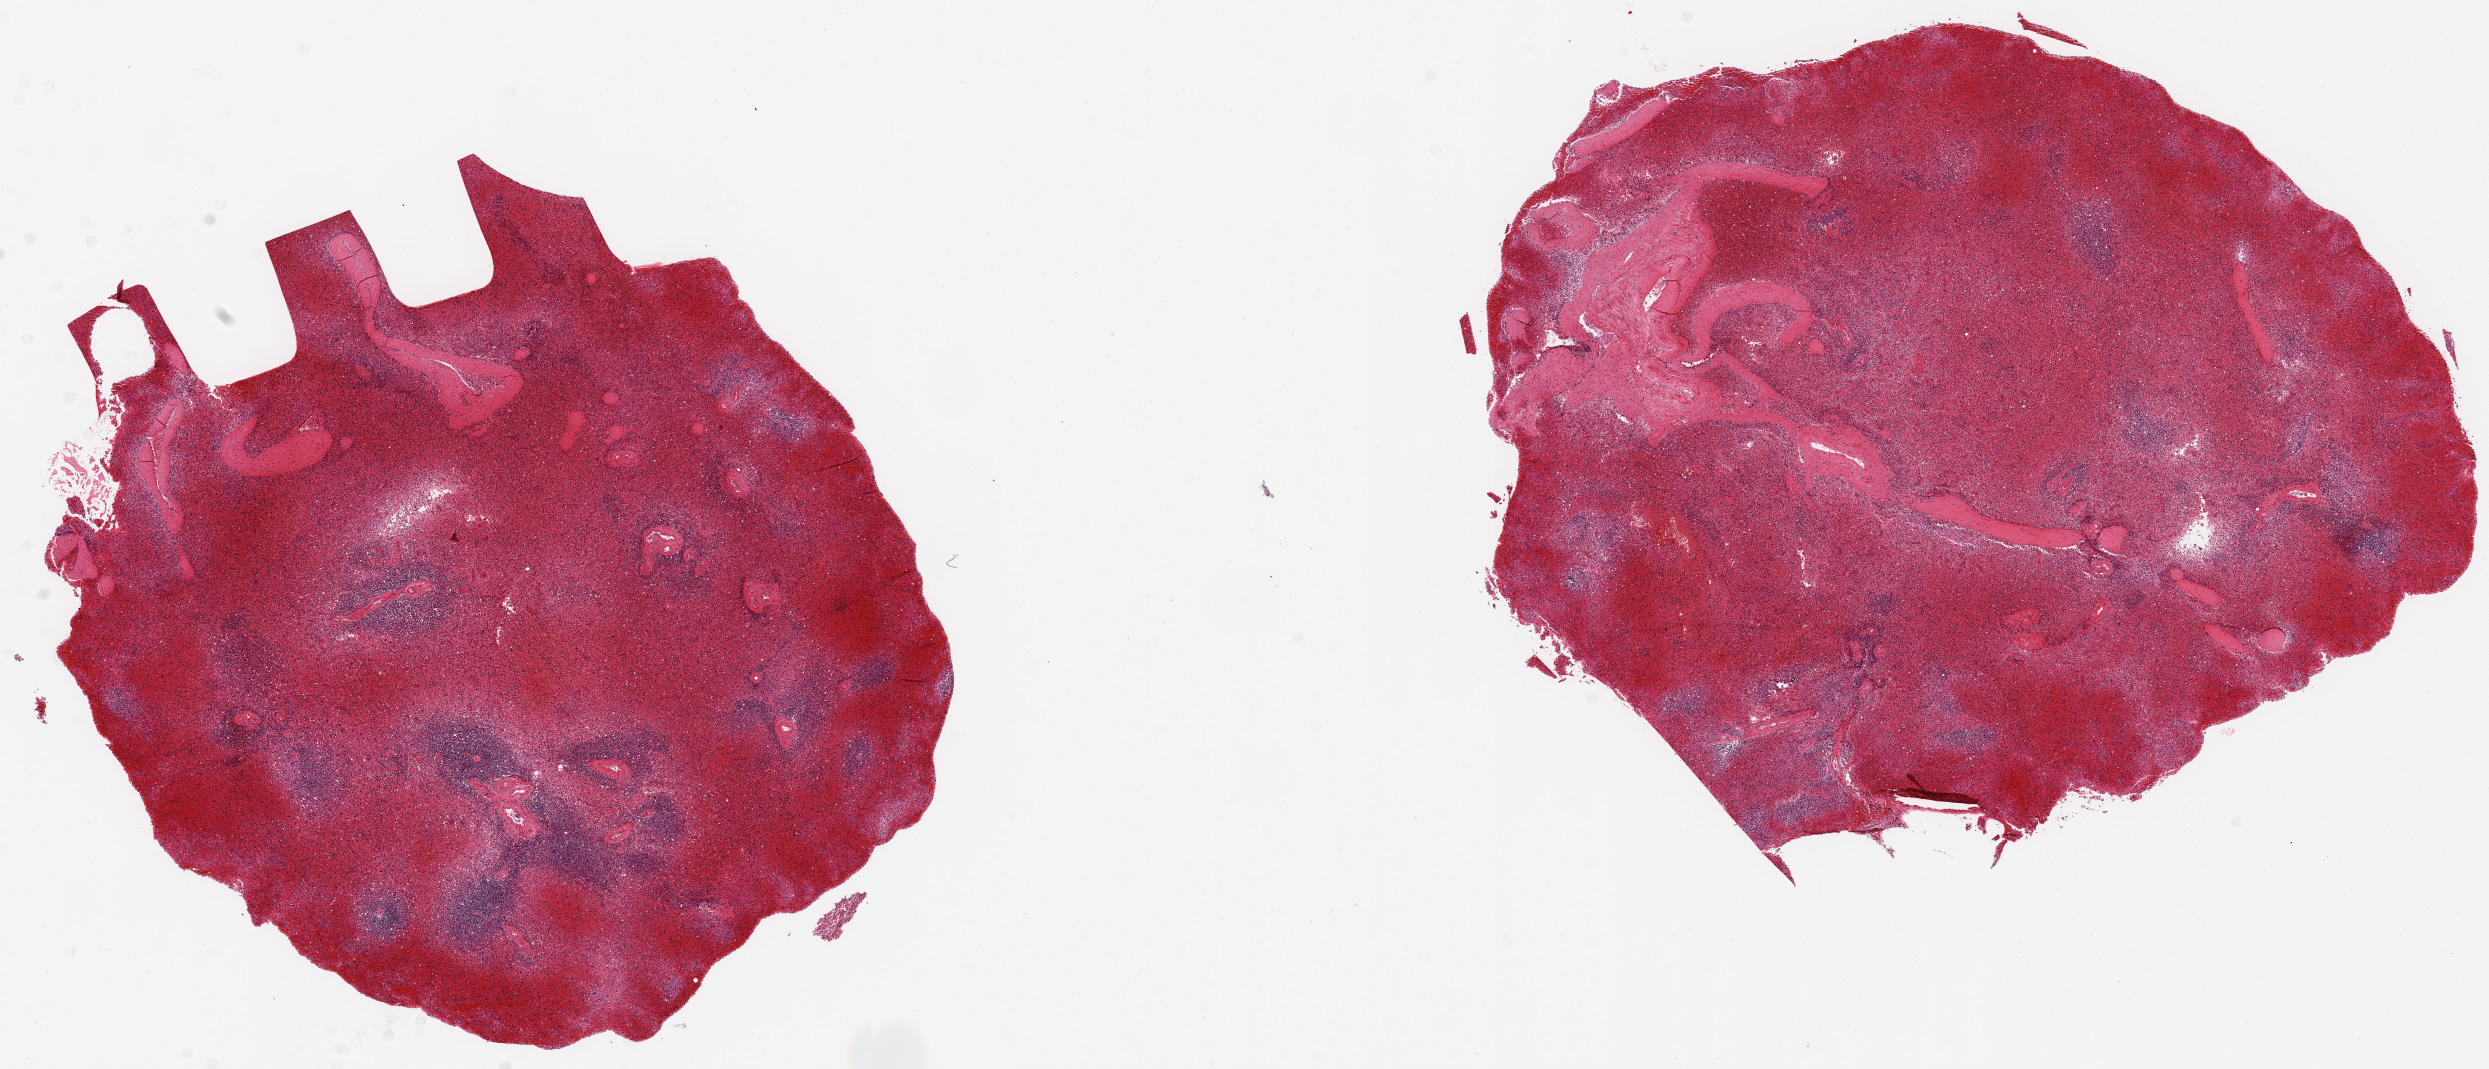
Whole-slide image, H&E stain, brightfield — whole scanned area (about 19.7 x 8.5 mm) shown as a low-resolution overview, PAXgene-fixed paraffin-embedded (PFPE) section, target tissue: spleen, donor tissue sample. Donor: male.
* review note (as recorded): 2 pieces ~6x6mm, badly autolyzed/congested